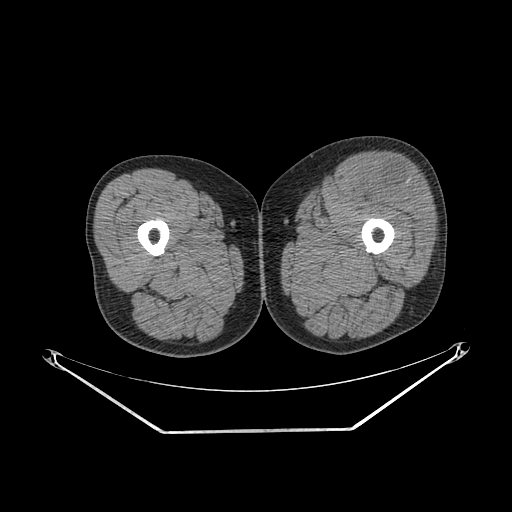
CT of an extremity soft-tissue mass (from a PET/CT study), one axial slice. Slice 228 of 267 in the series (ordered by position). 140 kVp. Soft-tissue window (W 400 / L 40 HU). 512 × 512 image matrix, field of view 500 × 500 mm. Male patient. From the clinical record (not read from this slice): histological type: extraskeletal osteosarcoma; grade: high; site of the primary tumour: thigh.
Structures marked on this image (expert contour drawn on MRI and transferred to this co-registered scan by the dataset authors):
- gross tumour volume (mass): bounding box [x1, y1, x2, y2] px = [361, 162, 424, 209]